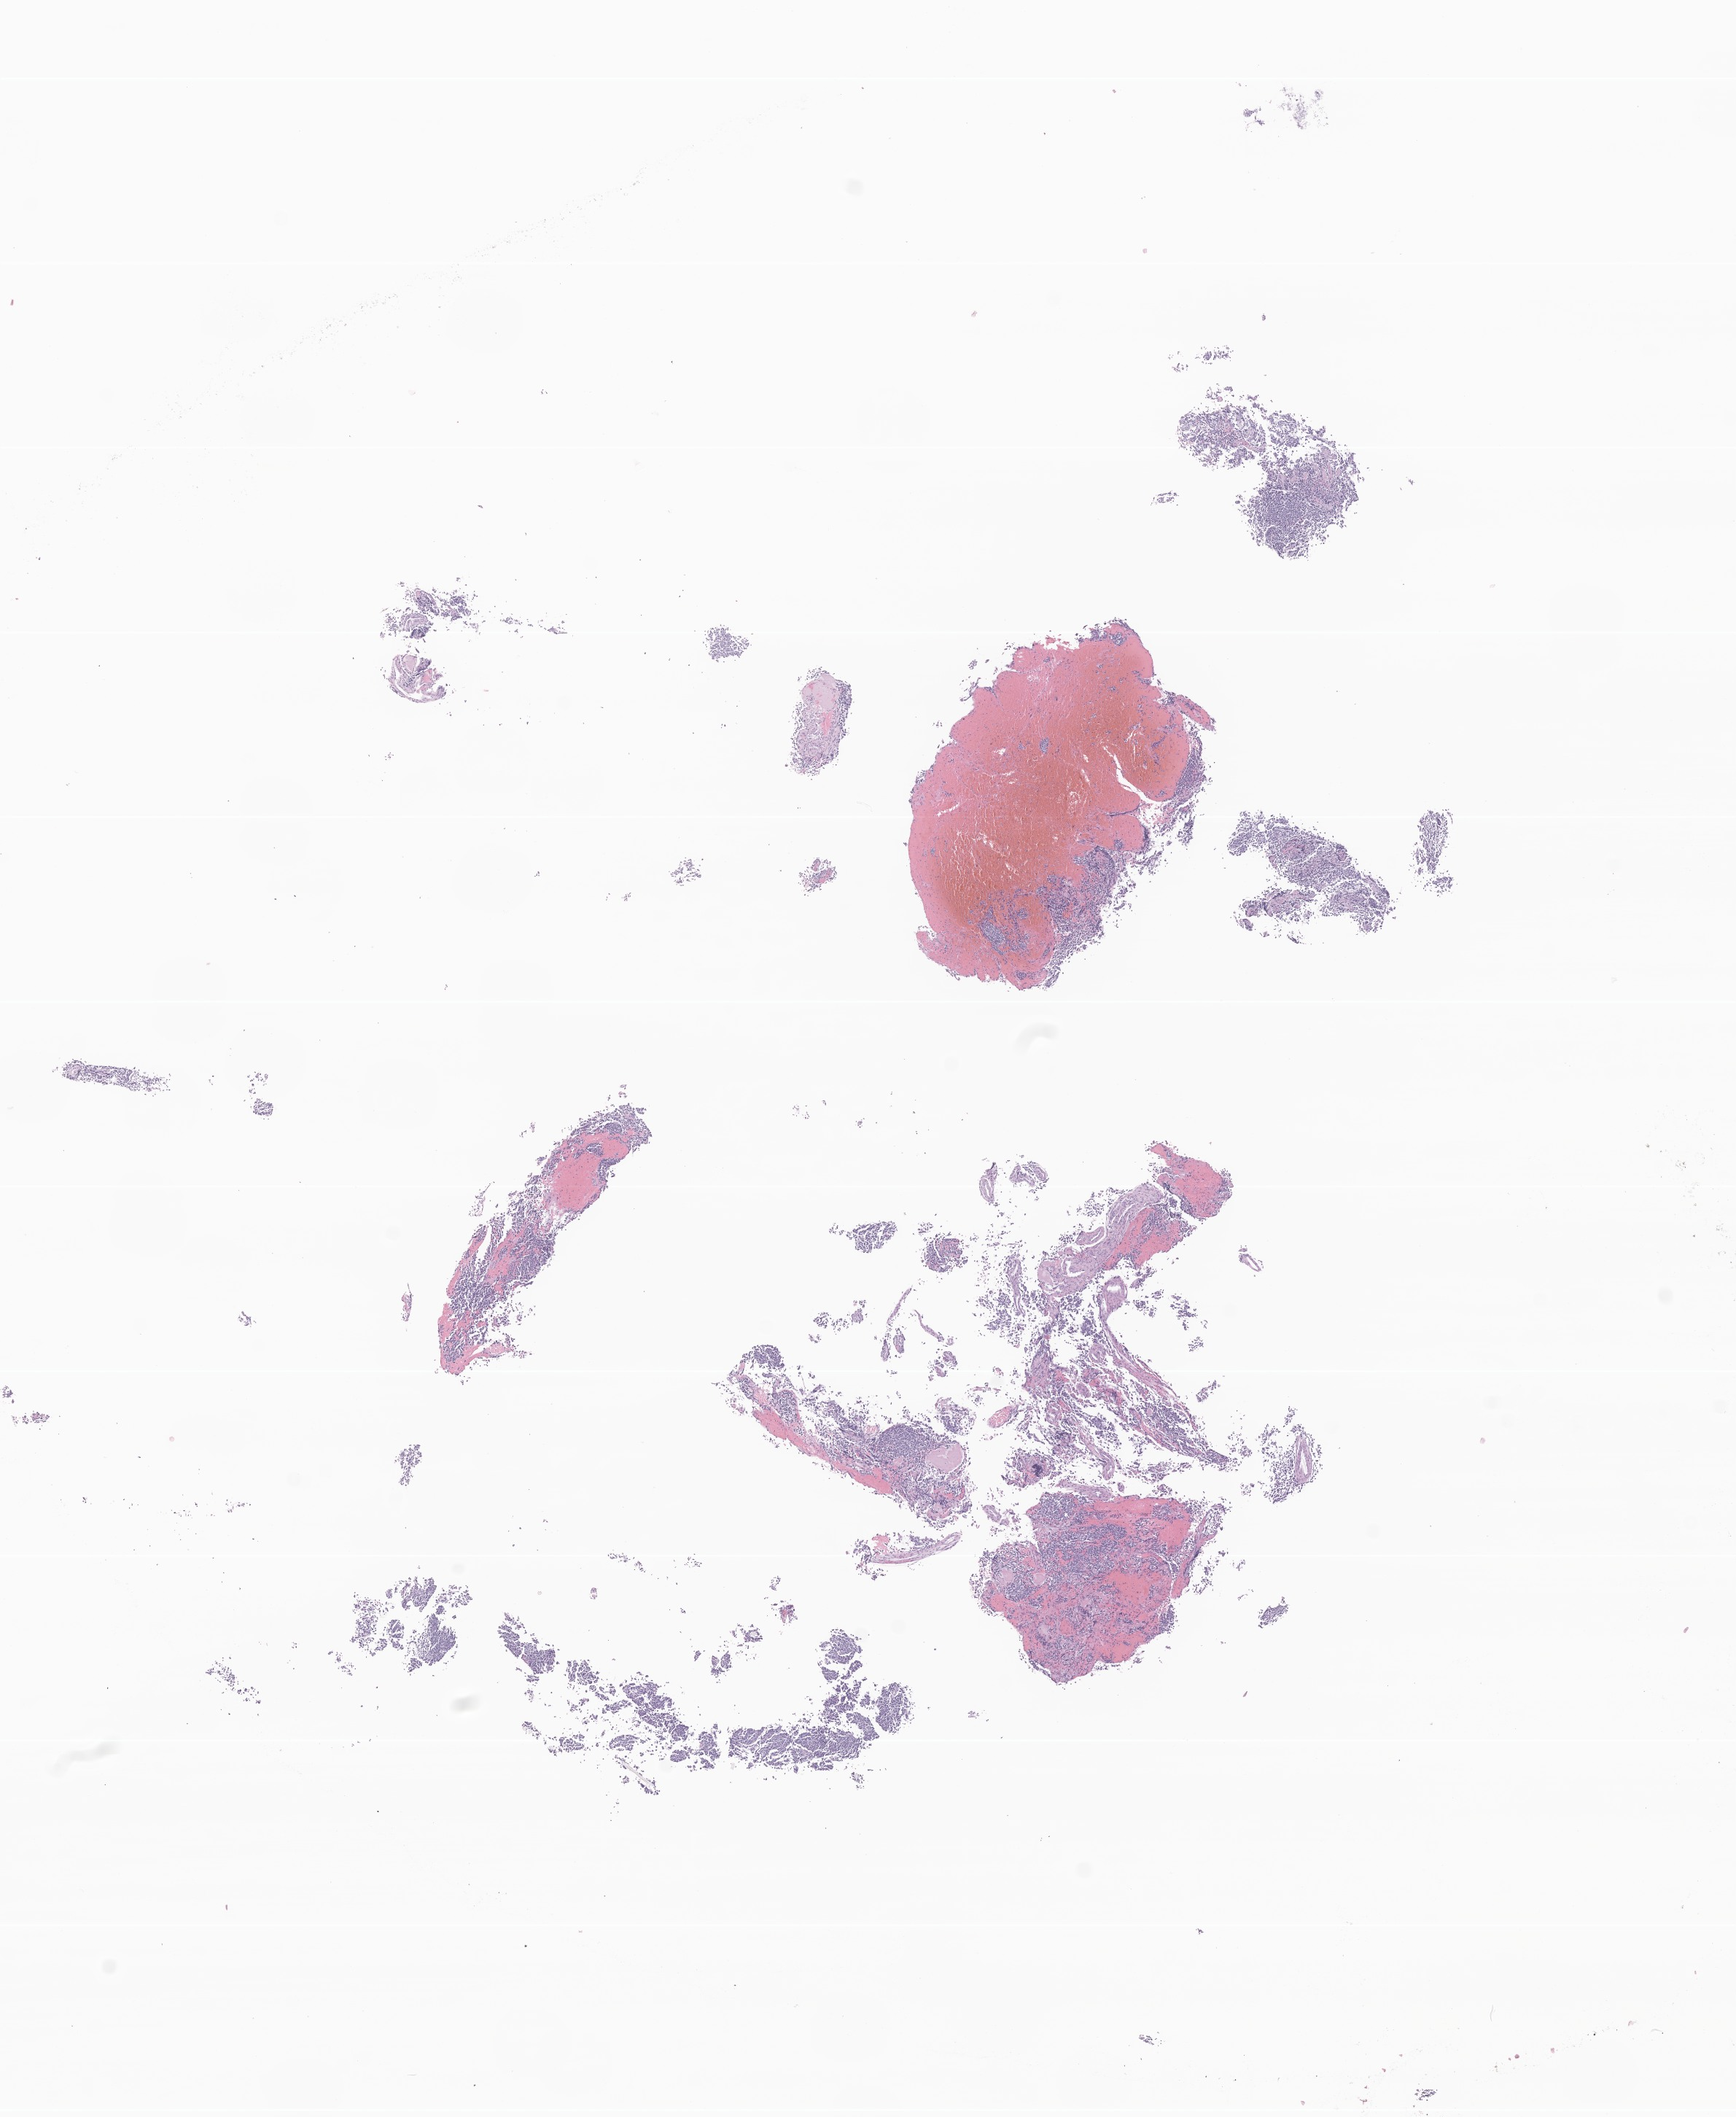
Whole-slide image, H&E stain of tumor tissue from the brain — low-resolution overview of the scanned area, about 10.0 x 12.2 mm. FFPE section. Female patient, age 57 months (4 years 9 months).
Diagnosis: Medulloblastoma, NOS.